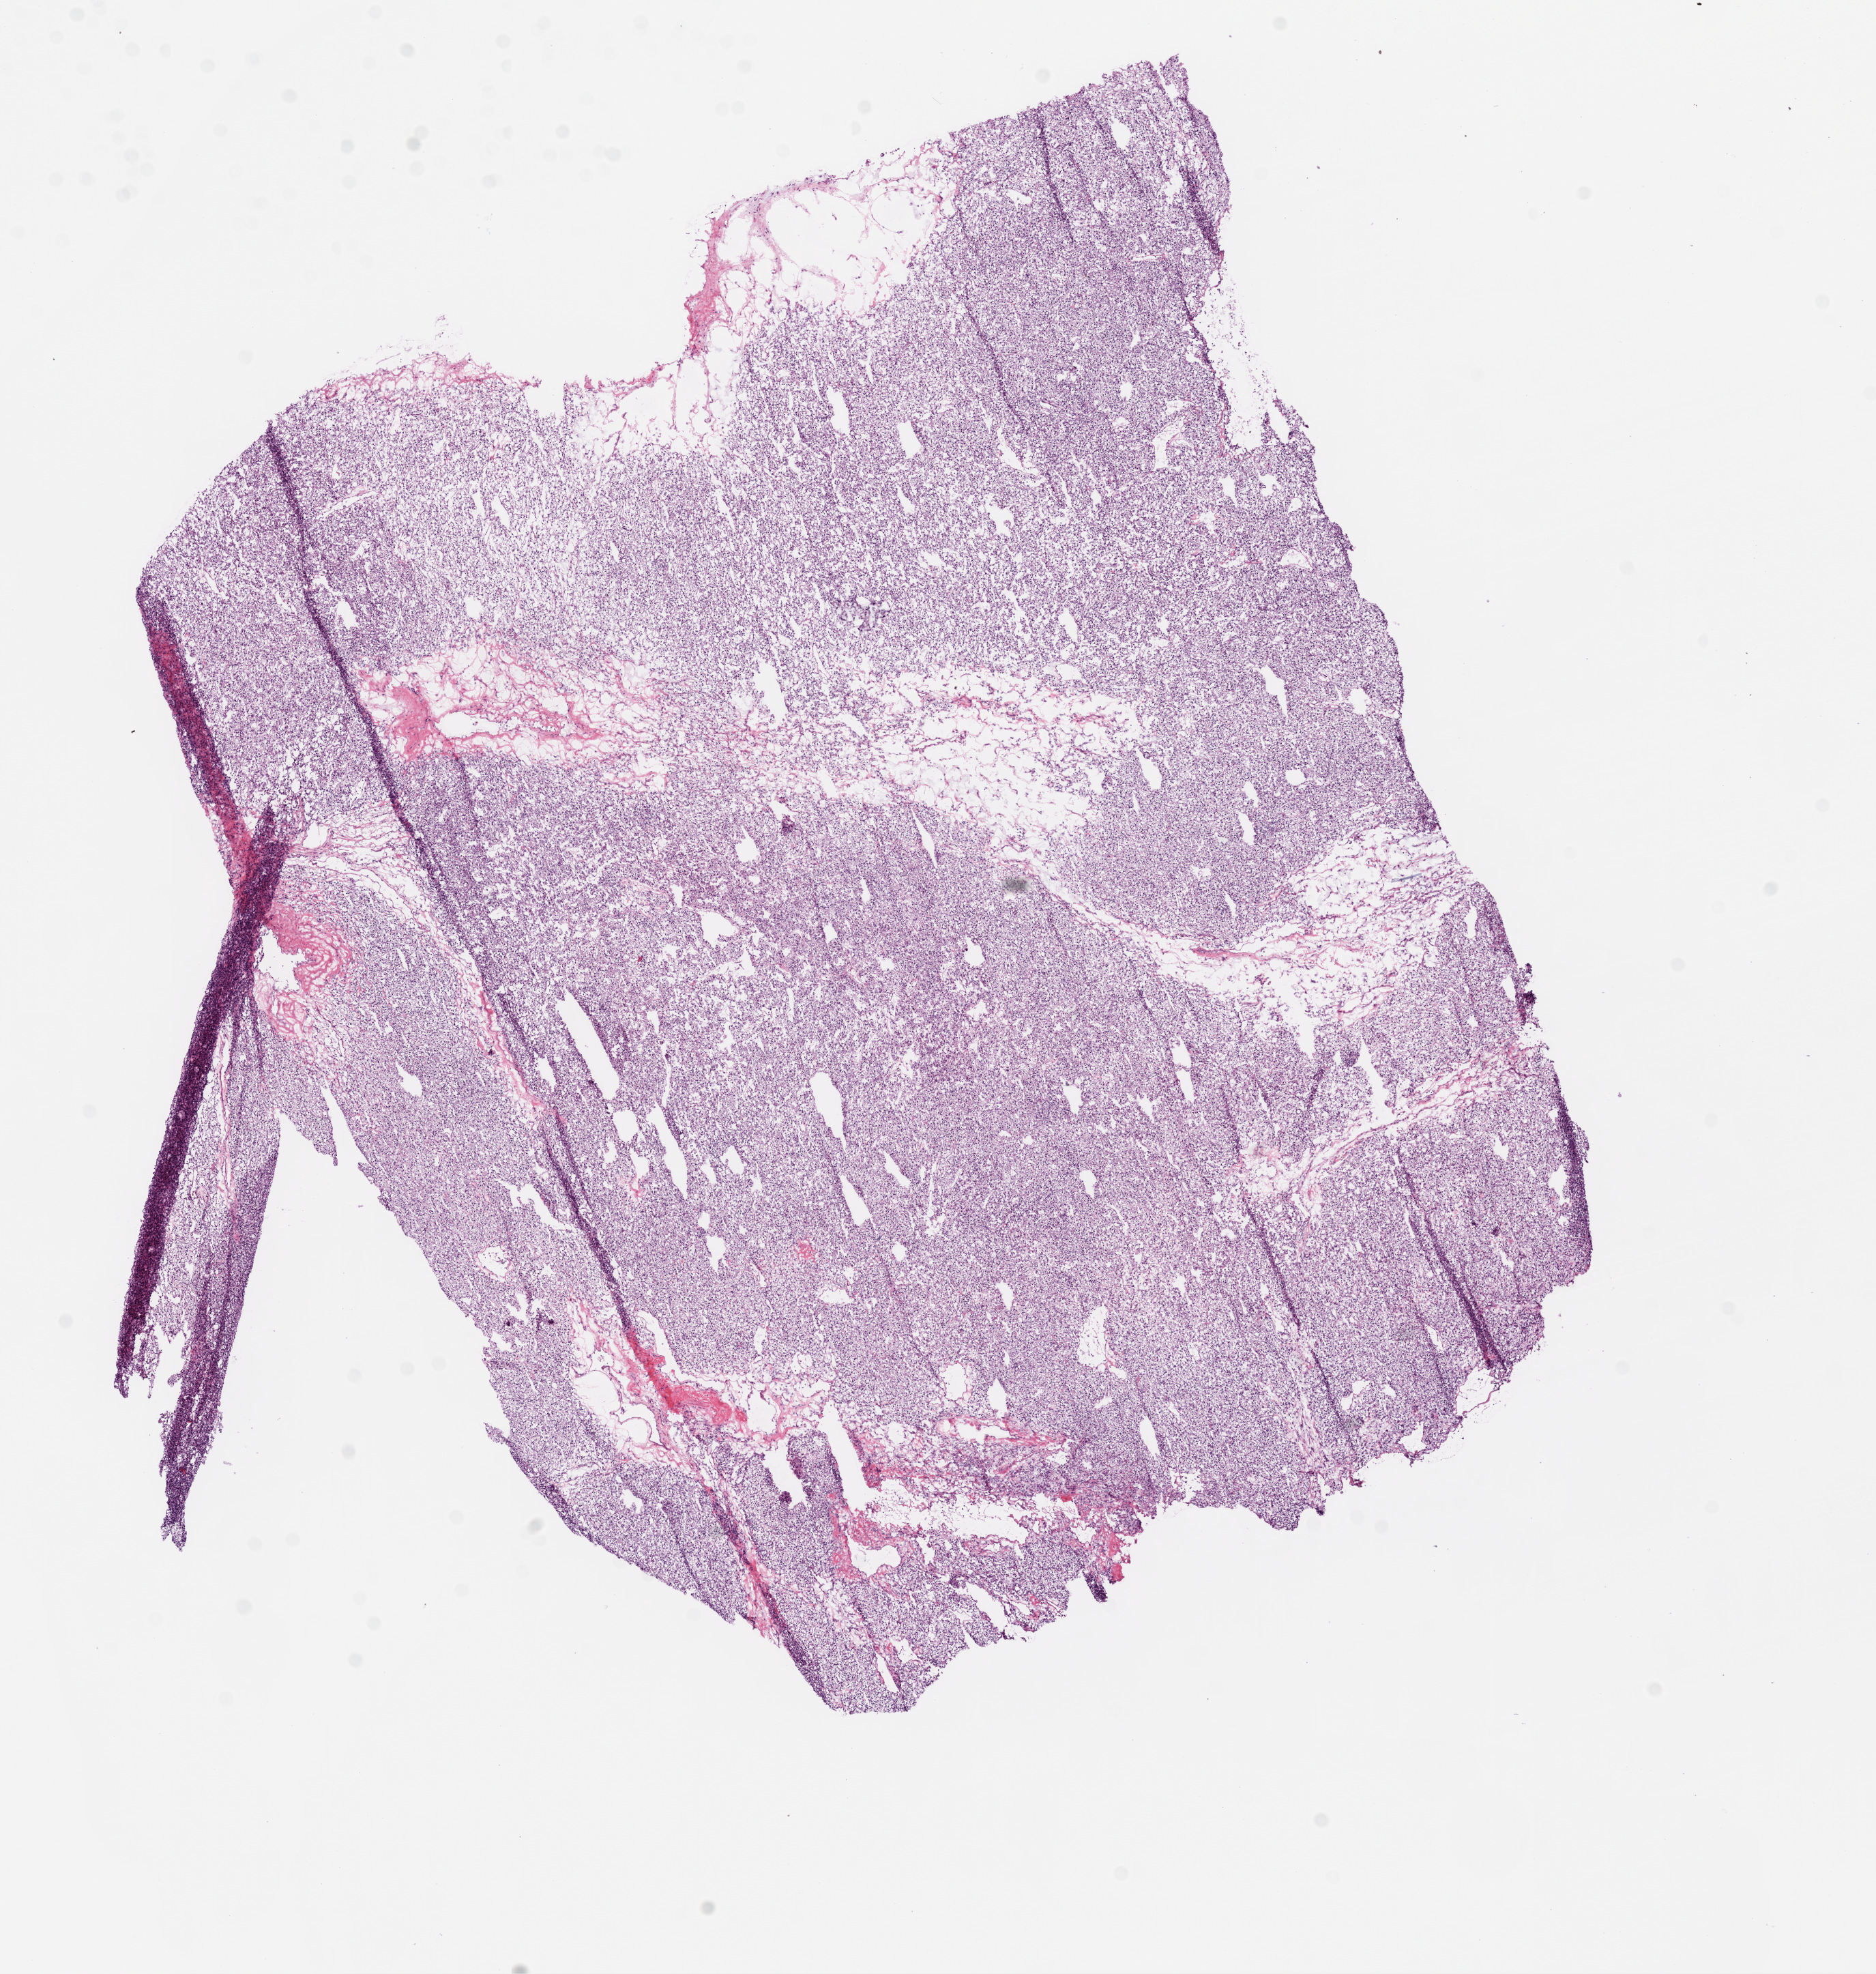
Whole-slide histology image, H&E-stained — low-resolution overview of the scanned area, about 11.0 x 11.6 mm. Frozen section. Sample: primary tumour, kidney. Female patient. Histologic grade: G2 (moderately differentiated). Slide review estimates, as recorded: tumour cells 93%, tumour nuclei 90%, normal cells 0%, stromal cells 5%, necrosis 2%.
- AJCC pathologic stage: I
- histologic diagnosis: Clear cell adenocarcinoma, NOS